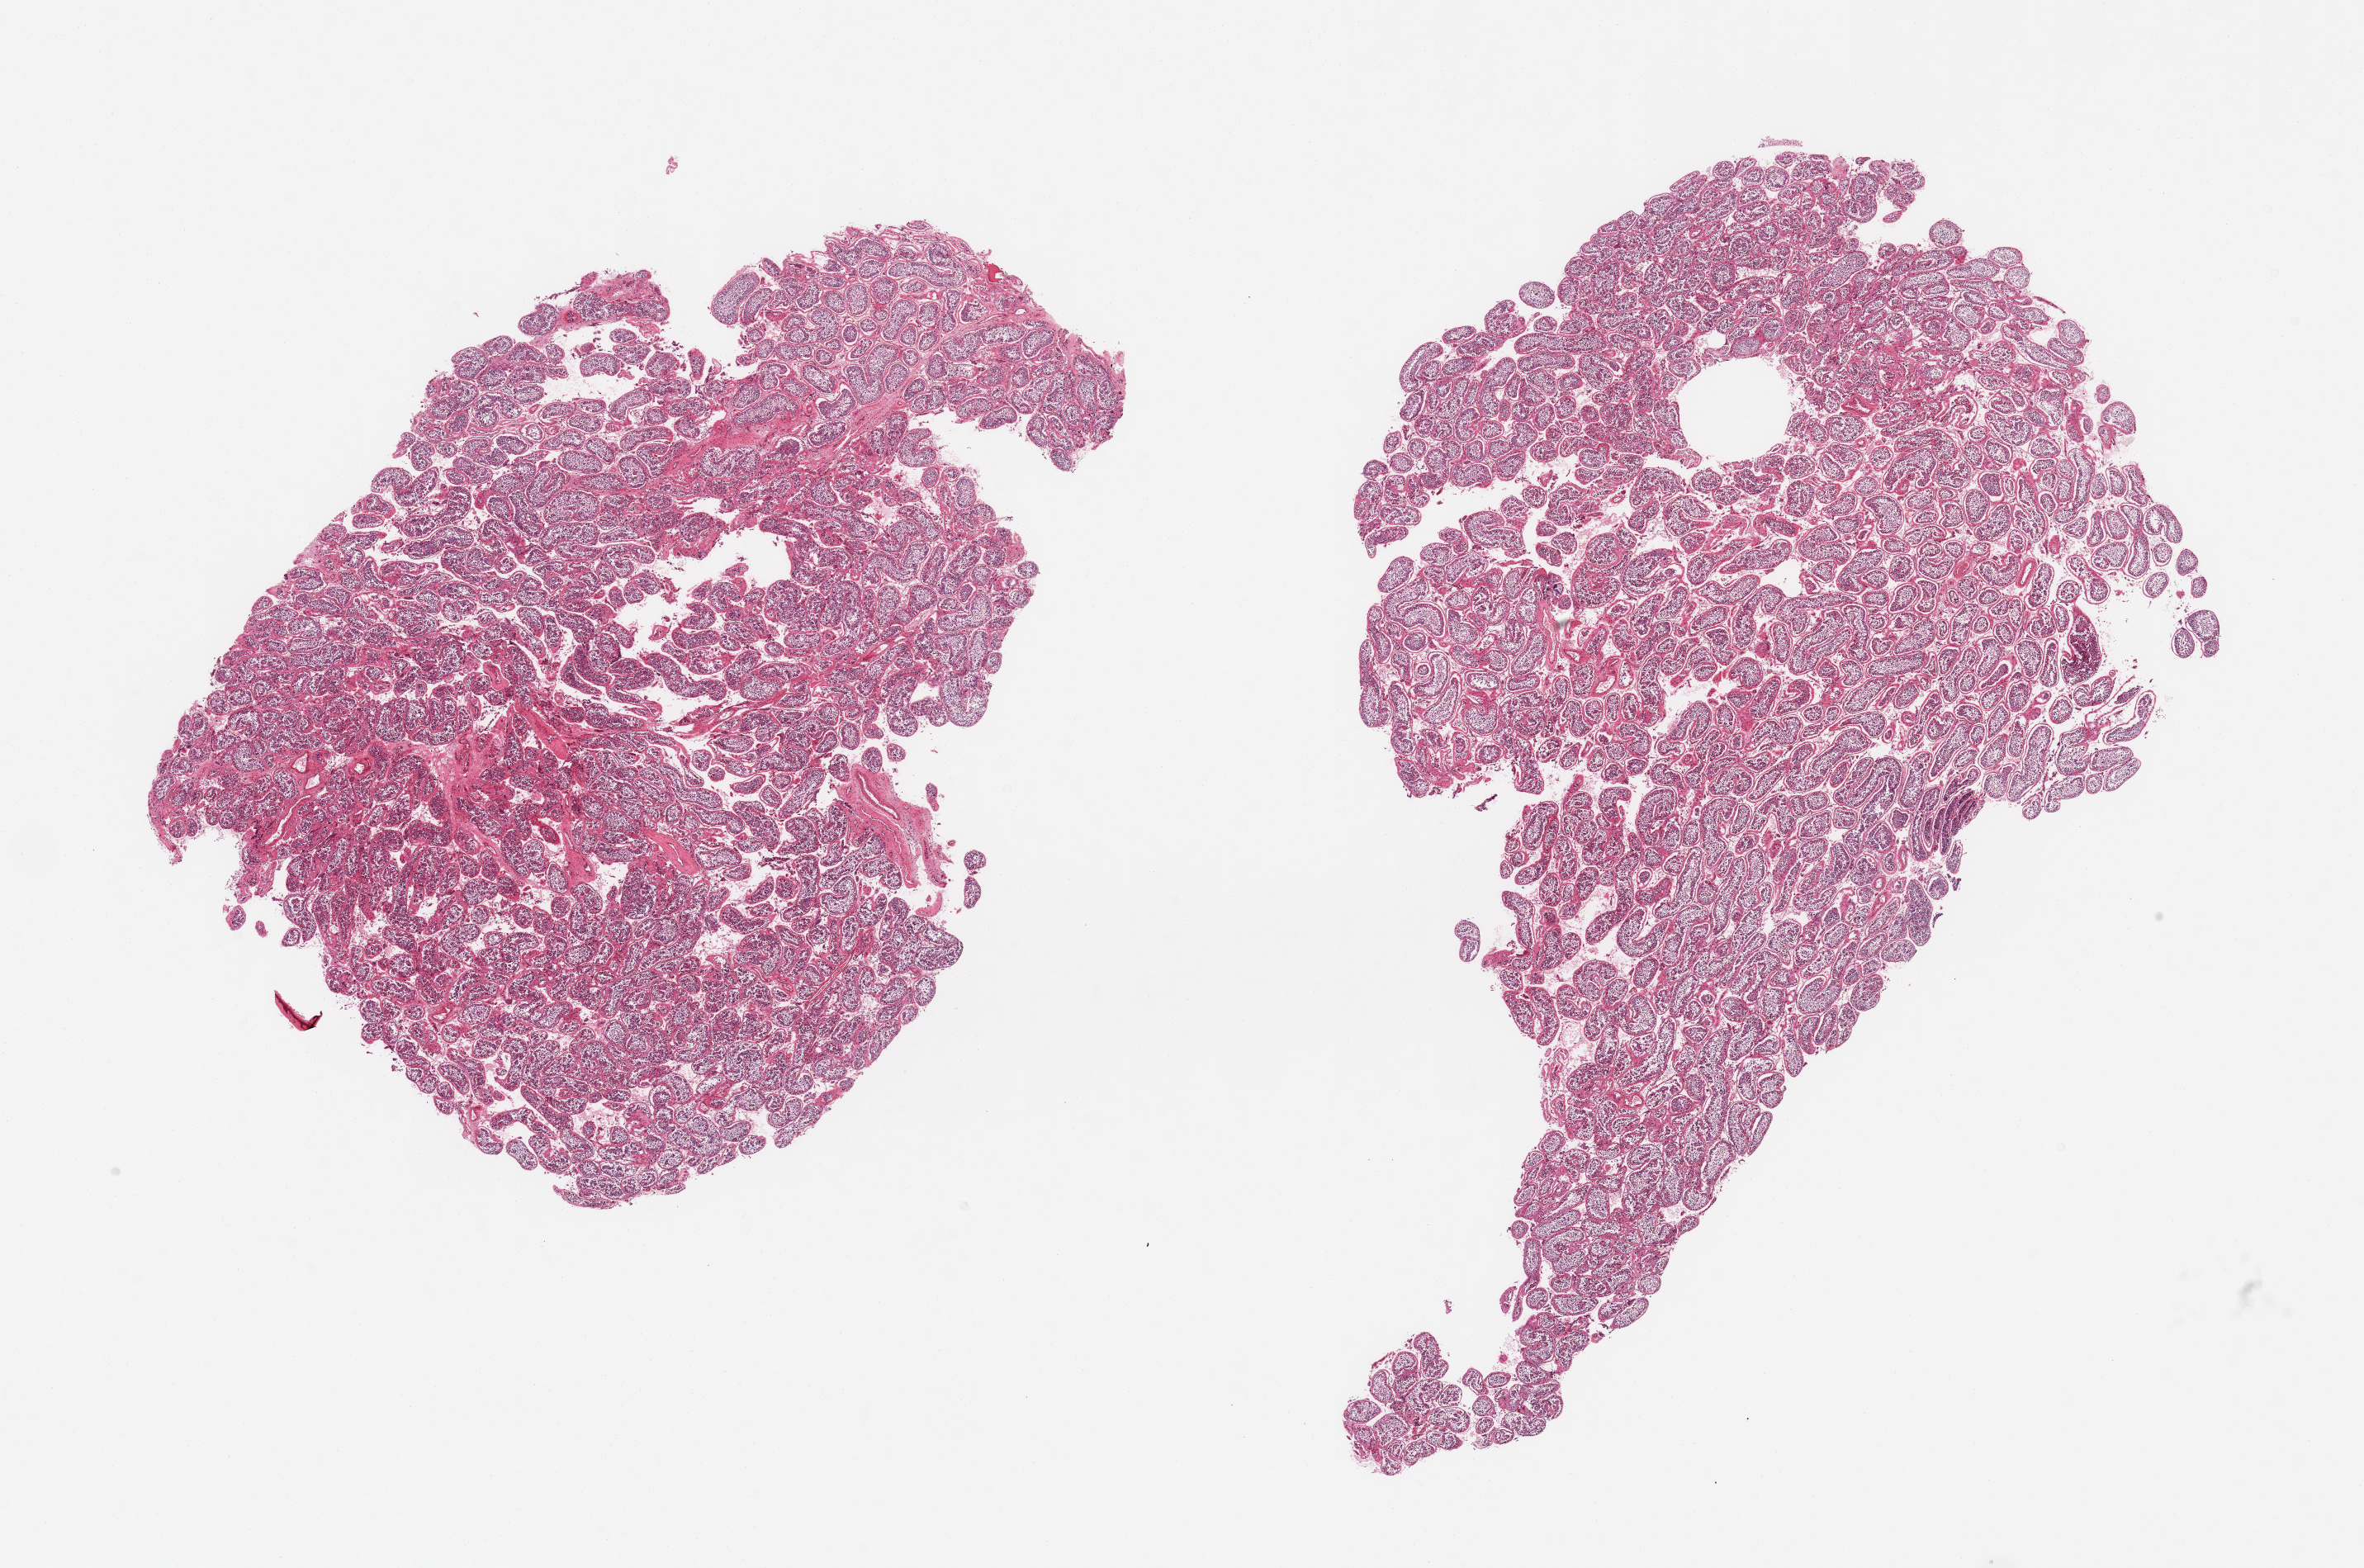
Hematoxylin and eosin (H&E) whole-slide image, whole scanned area (about 22.6 x 15.0 mm) shown as a low-resolution overview; PAXgene-fixed paraffin-embedded (PFPE) section; target tissue: testis; donor tissue sample. Male donor.
Review note (as recorded): 2 pieces, spermatogenesis is present.